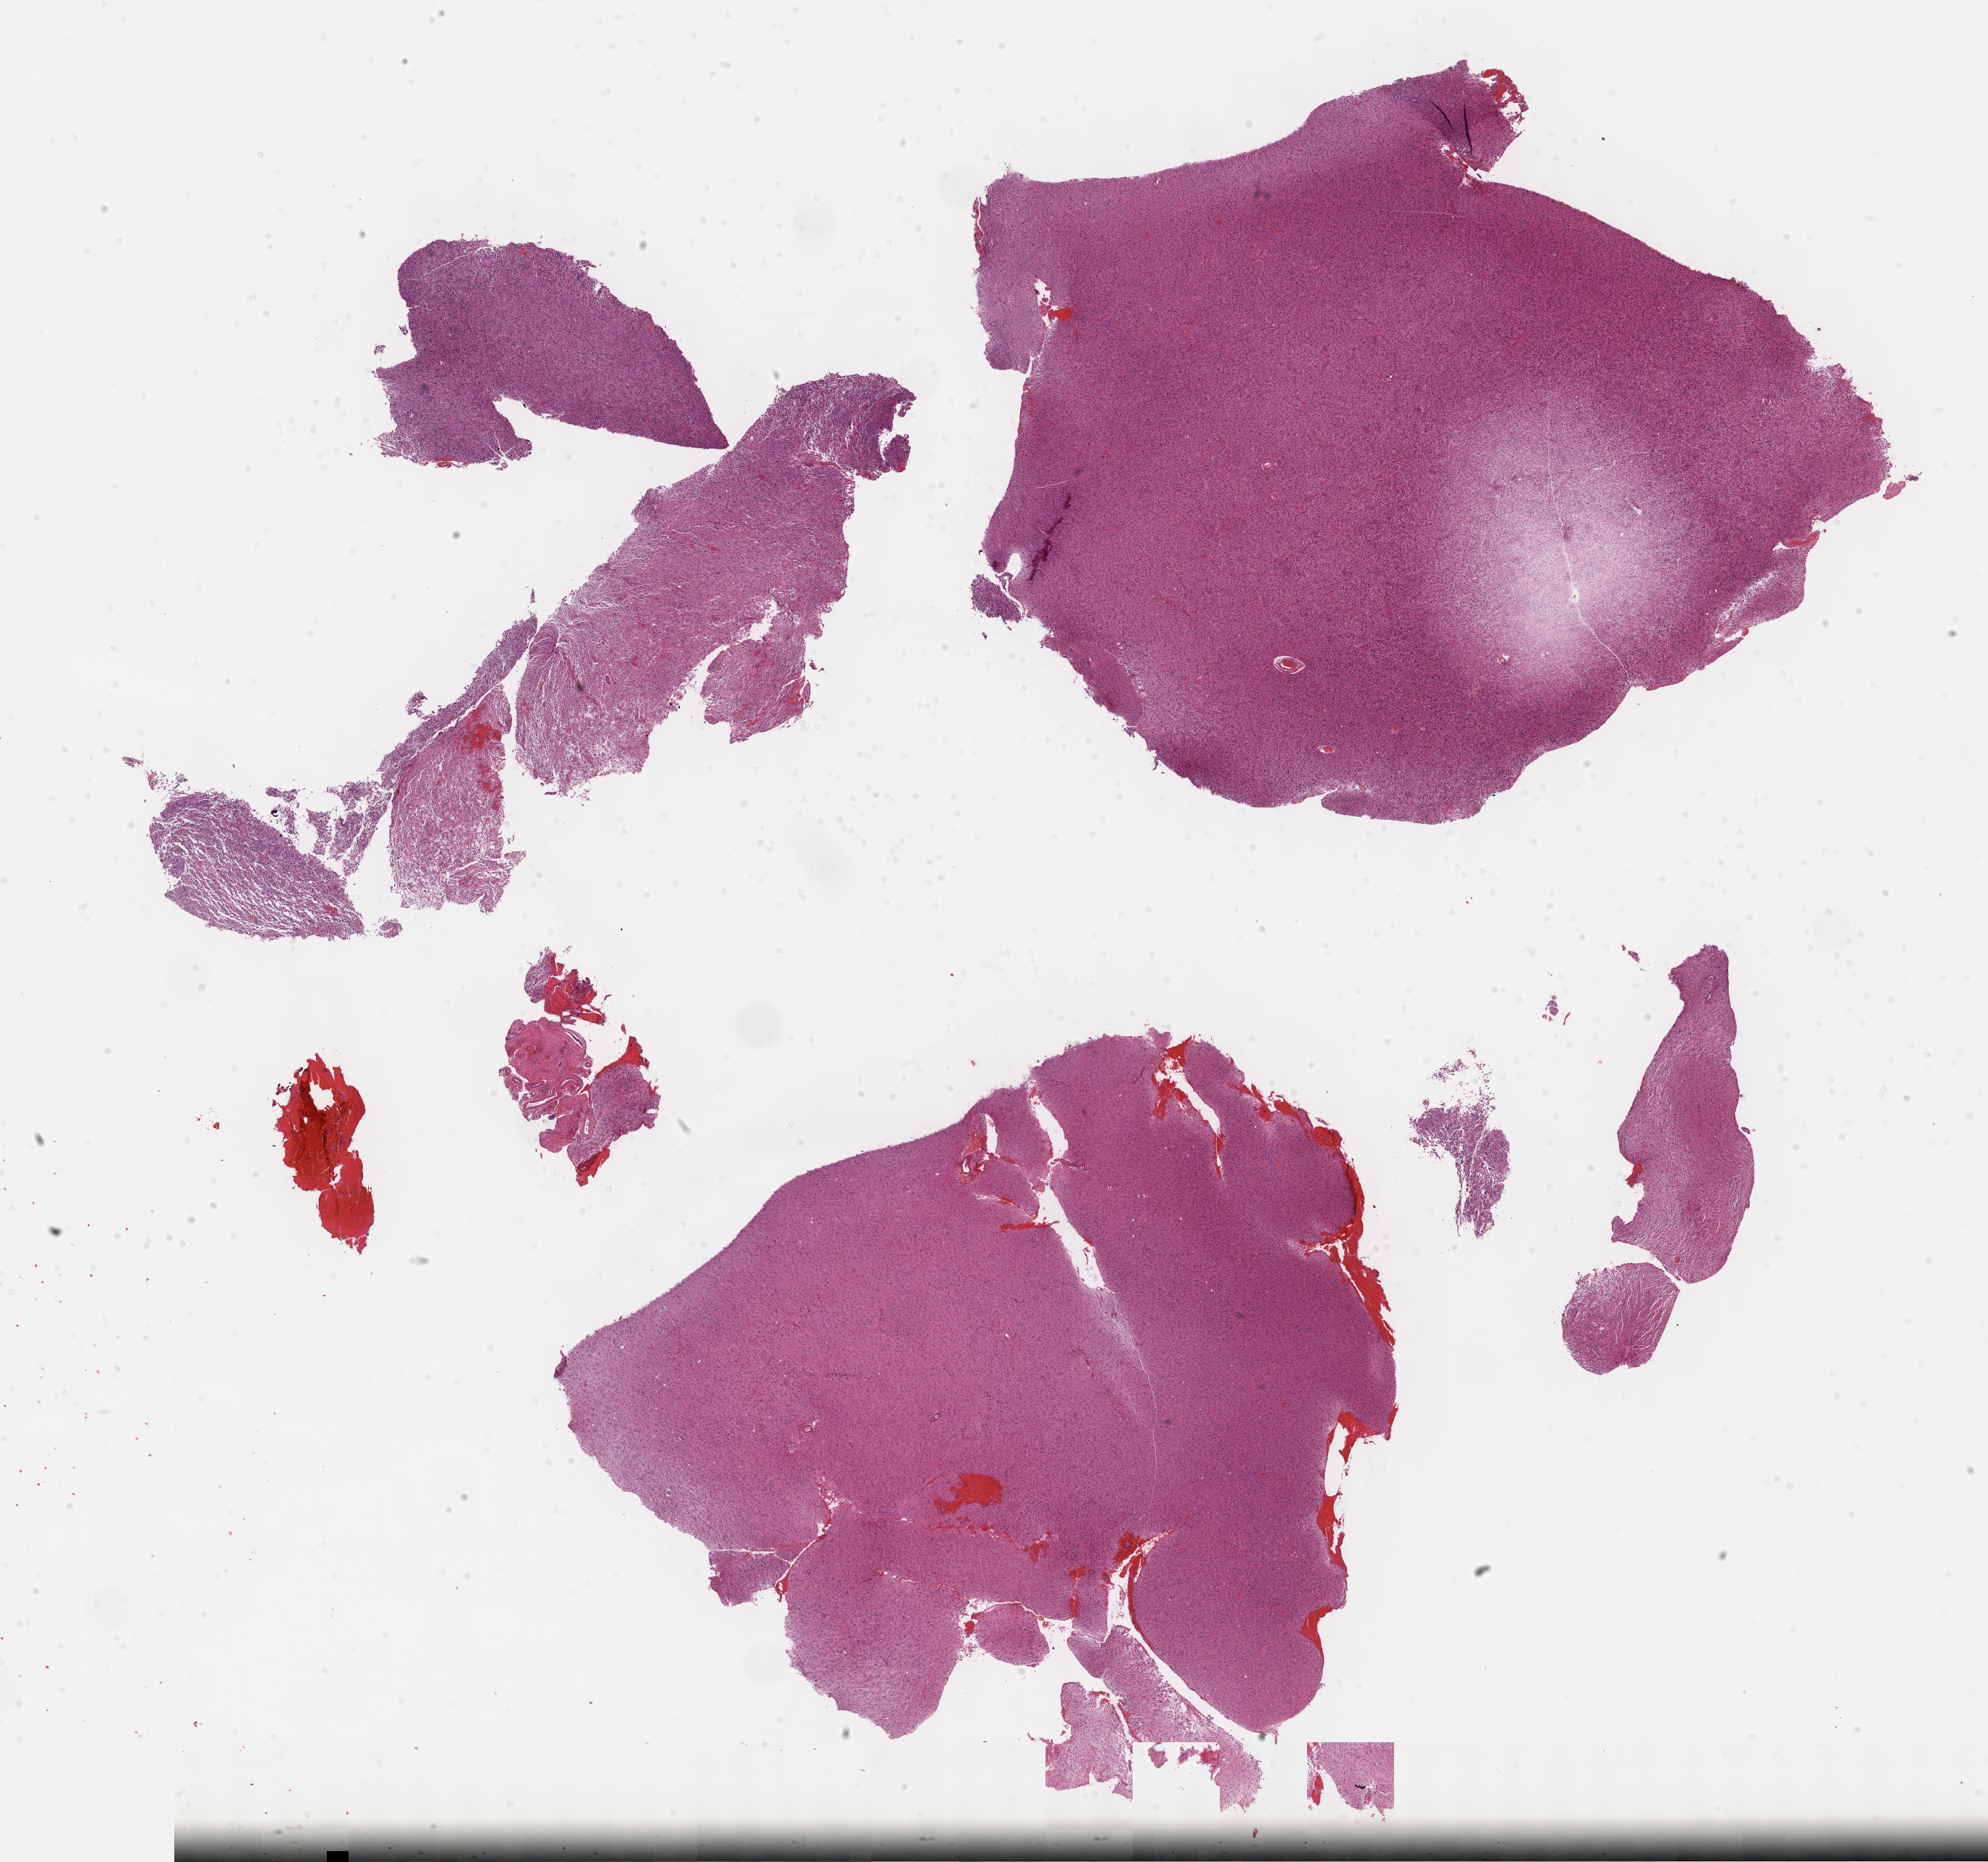
Digitized H&E tissue section (whole slide) — whole scanned area (about 22.1 x 20.7 mm, acquisition: 40x scan) shown as a low-resolution overview; formalin-fixed paraffin-embedded (FFPE) diagnostic section; brain, primary tumour sample. Patient: female, age at initial diagnosis 29 years. Histologic grade: G3 (poorly differentiated).
Histologic diagnosis: Astrocytoma, anaplastic (cerebrum). Laterality: left.